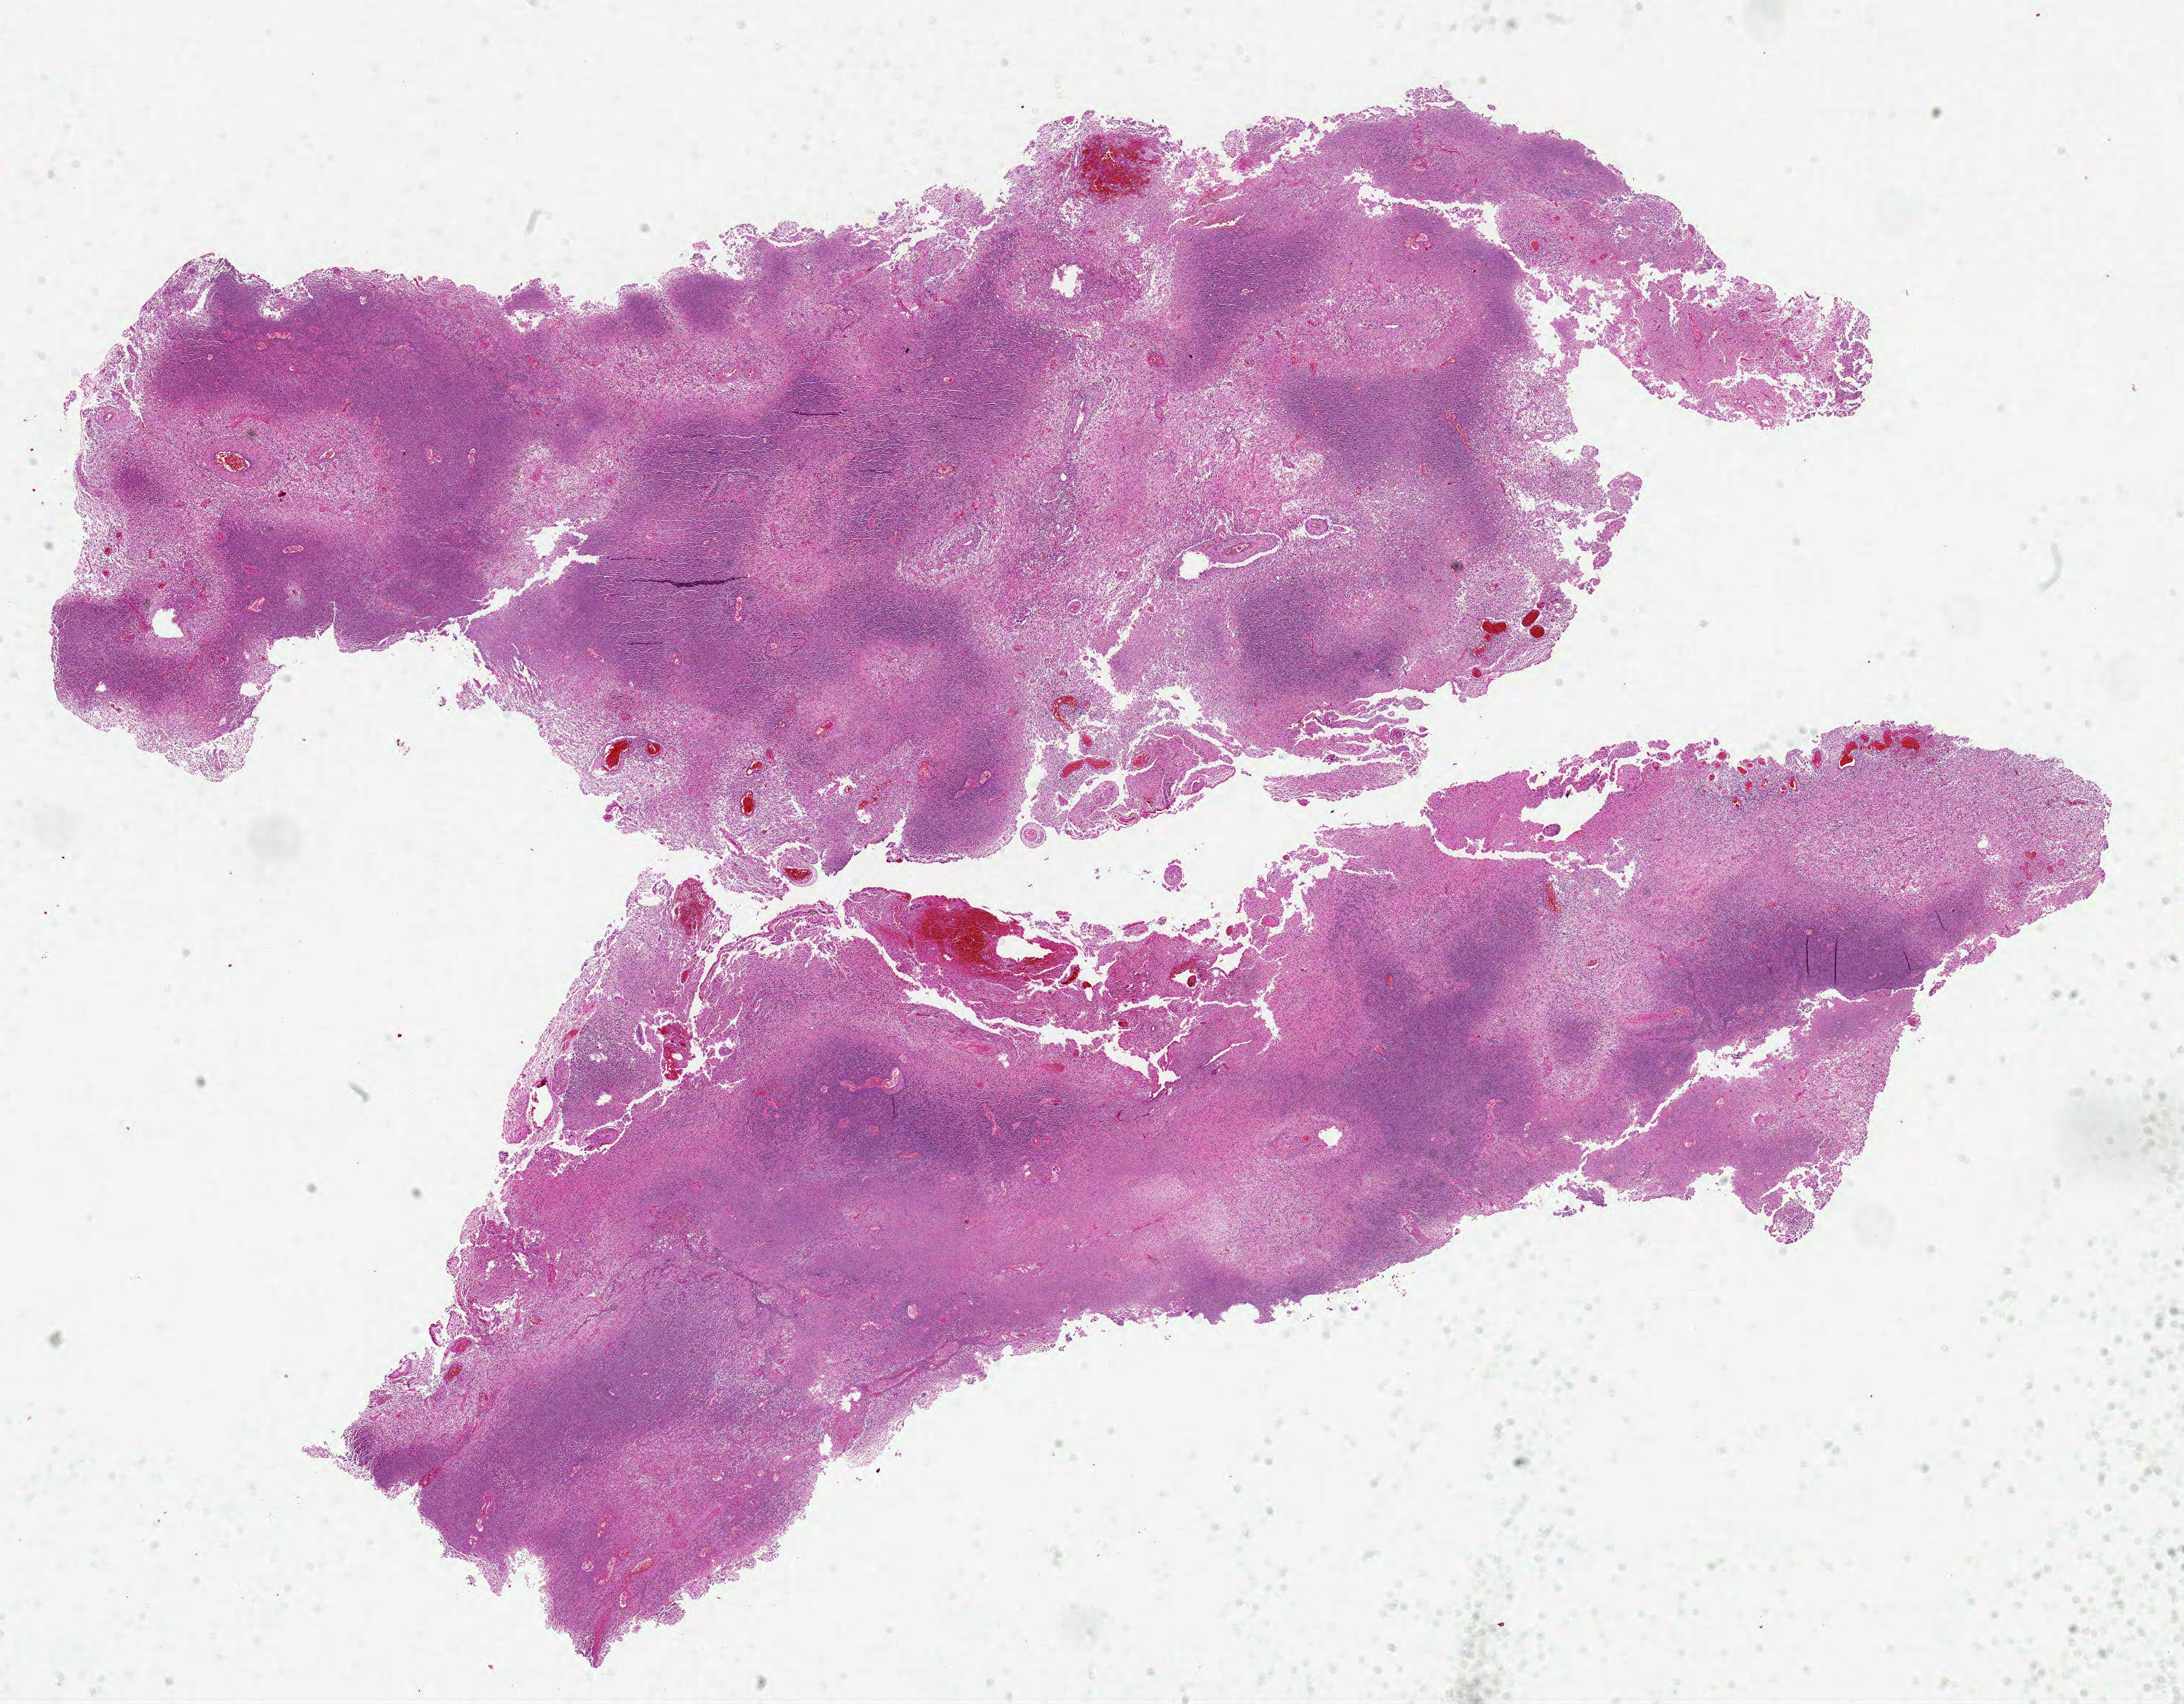
Whole-slide histology image, H&E, a low-resolution overview of the entire scanned area, about 24.0 x 18.7 mm, formalin-fixed paraffin-embedded (FFPE) diagnostic section, sample: primary tumour, brain. Female, age 75 years at initial diagnosis.
Pathologic diagnosis: Glioblastoma.